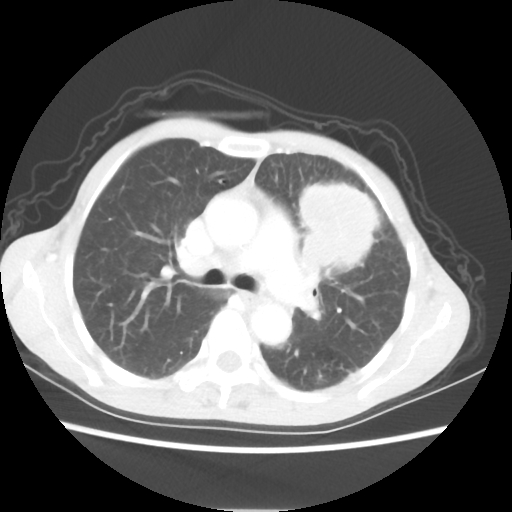
Chest CT, one axial slice. Slice 38 of 56 in the series (ordered by position). Reconstruction kernel STANDARD. 80 kVp. Lung window (W 1500 / L -600 HU). 5 mm slice thickness. 512 × 512 image matrix. Patient: female, 60 years. Case-level facts recorded for this patient, not image findings: clinical TNM (as recorded): T4 N1 M0.
Structures marked on this image (bounding box drawn by a radiologist):
- lung tumour (recorded histology: adenocarcinoma): bounding box (x1, y1, x2, y2) in pixels: (300, 185, 372, 283)